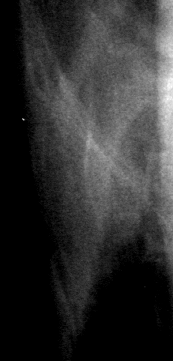
Region of interest cut from a scanned film mammogram (one marked finding); right breast; CC view; BI-RADS breast density category 3 (scale 1–4).
Mass, shape architectural distortion; BI-RADS assessment category 2; pathology result (as recorded, not read from the image): benign.